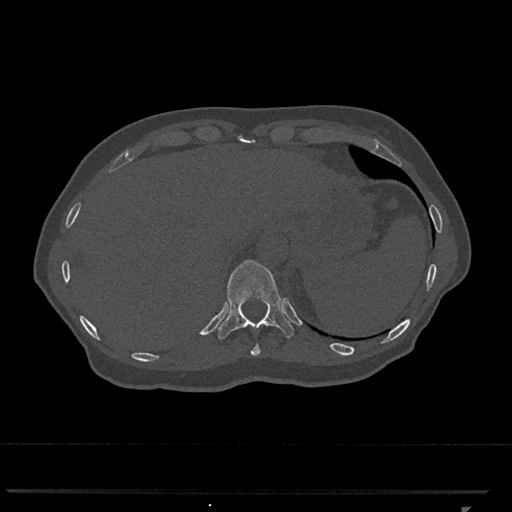
CT including the spine, one axial slice. Slice 527 of 793 in the series (ordered by position). Reconstruction kernel Br40s/3. Bone window (W 1800 / L 400 HU). 0.5 mm slice thickness. 512 × 512 image matrix. Patient: female, 62 years. Case-level facts recorded for this patient, not image findings: primary cancer: renal.
Outlined on this slice (semi-automatically segmented with operator editing):
- T10 vertebra: bounding box (x1, y1, x2, y2) in pixels: (250, 343, 261, 356)
- T11 vertebra: (217, 260, 294, 340)